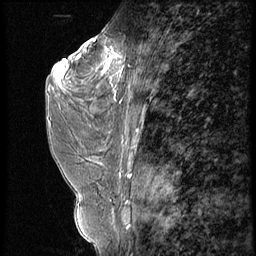
Breast MRI (dynamic contrast-enhanced), one sagittal slice. Slice 30 of 56 in the series (ordered by position). 4 images stored at this slice position (order not interpretable as contrast timing). 1.5 T. TE 4.2 ms, TR 9 ms. 2.5 mm slice thickness. 256 × 256 image matrix, field of view 180 × 180 mm. Patient: female, 44 years. From the clinical record (not read from this slice): setting: breast cancer imaged before/during neoadjuvant chemotherapy; receptor status: triple-negative.
Outlined on this slice (semi-automatic segmentation, software-assisted and operator-edited):
- analysis volume of interest (the breast-tissue region the enhancement analysis was run in; not a lesion): bounding box [x1, y1, x2, y2] px = [87, 28, 132, 99]
- tumour enhancement mask (voxels above the 140 % enhancement threshold inside the analysis volume of interest): [102, 46, 123, 73]